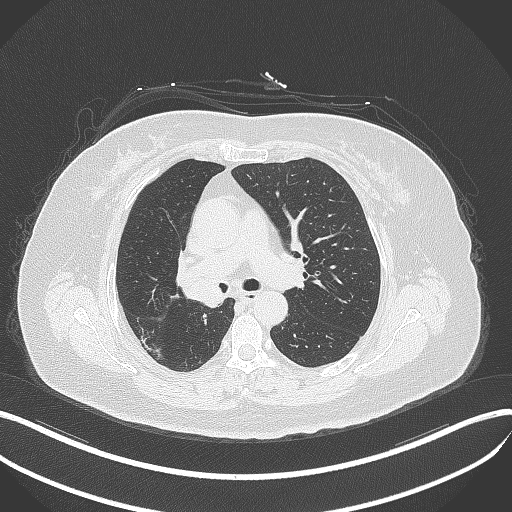
Chest CT, one axial slice. Position 224 of 376 along the scan axis. 120 kVp. Lung window (W 1500 / L -600 HU). 1 mm slice thickness. 512 × 512 image matrix, field of view 400 × 400 mm. Female patient, age 60 years. Case-level facts recorded for this patient, not image findings: clinical TNM (as recorded): T1c N0 M0.
Annotated regions visible in this slice (bounding box drawn by a radiologist):
- lung tumour (recorded histology: squamous cell carcinoma): bounding box (x1, y1, x2, y2) in pixels: (167, 253, 225, 309)